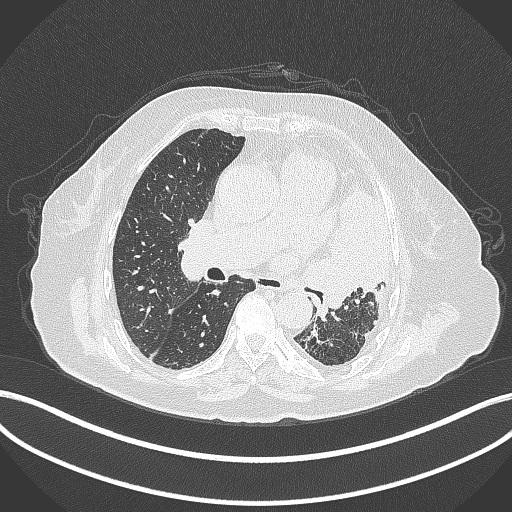
Chest CT, one axial slice; position 205 of 399 along the scan axis; lung window (W 1500 / L -600 HU); 1 mm slice thickness; 512 × 512 image matrix. Patient: female, 75 years. From the clinical record (not read from this slice): clinical TNM (as recorded): T3 N3 M1.
Annotated regions visible in this slice (rectangle marked by the reading radiologist):
- lung tumour (recorded histology: adenocarcinoma): box from (x=301, y=189) to (x=391, y=312) px